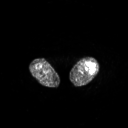
FDG PET of an extremity soft-tissue mass (from a PET/CT study), one axial slice. Position 198 of 267 along the scan axis. 3.27 mm slice thickness. 128 × 128 image matrix, field of view 700 × 700 mm. Patient: female, 62 years. From the clinical record (not read from this slice): histological type: undifferentiated – high grade; grade: high; site of the primary tumour: left thigh.
Structures marked on this image (expert contour drawn on MRI and transferred to this co-registered scan by the dataset authors):
- gross tumour volume including surrounding oedema: box from (x=84, y=62) to (x=95, y=72) px